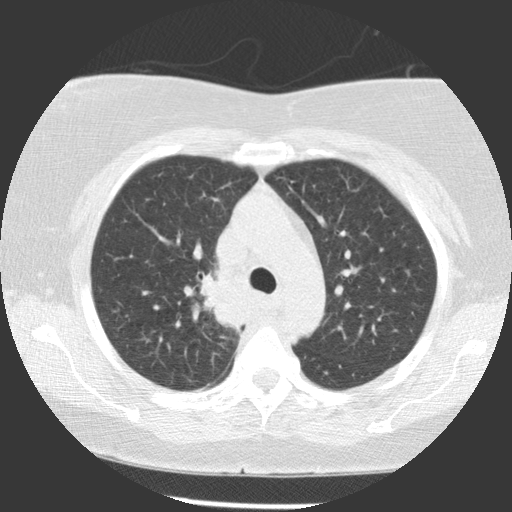
Low-dose screening chest CT, one axial slice; position 83 of 116 along the scan axis; 140 kVp; lung window (W 1500 / L -600 HU); 2.5 mm slice thickness; 512 × 512 image matrix, field of view 320 × 320 mm.
Outlined on this slice (outlined manually by an expert reader):
- lesion 1 (tumor, upper lobe of right lung): bounding box (x1, y1, x2, y2) in pixels: (200, 271, 246, 333)